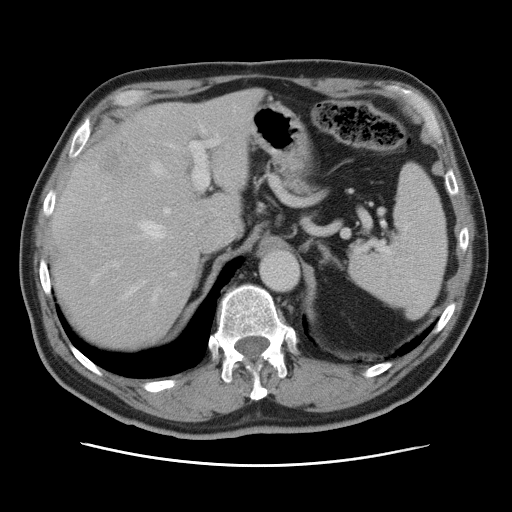
Contrast-enhanced abdominal CT, one axial slice; slice 56 of 80 in the series (ordered by position); 120 kVp; intravenous contrast given; soft-tissue window (W 400 / L 40 HU); 5 mm slice thickness; 512 × 512 image matrix, field of view 370 × 370 mm. Male patient, age 69 years. Case-level facts recorded for this patient, not image findings: diagnosis: colorectal cancer liver metastases, imaged before liver resection; multiple liver metastases: no.
Outlined on this slice (manually delineated by an expert):
- hepatic veins: bounding box <125,125,206,301> (left, top, right, bottom; pixels)
- liver: <52,92,259,351>
- planned liver remnant (the part of the liver to remain after resection): <51,92,259,351>
- portal vein (with intrahepatic branches): <112,132,222,276>
- liver metastasis: <105,146,122,175>